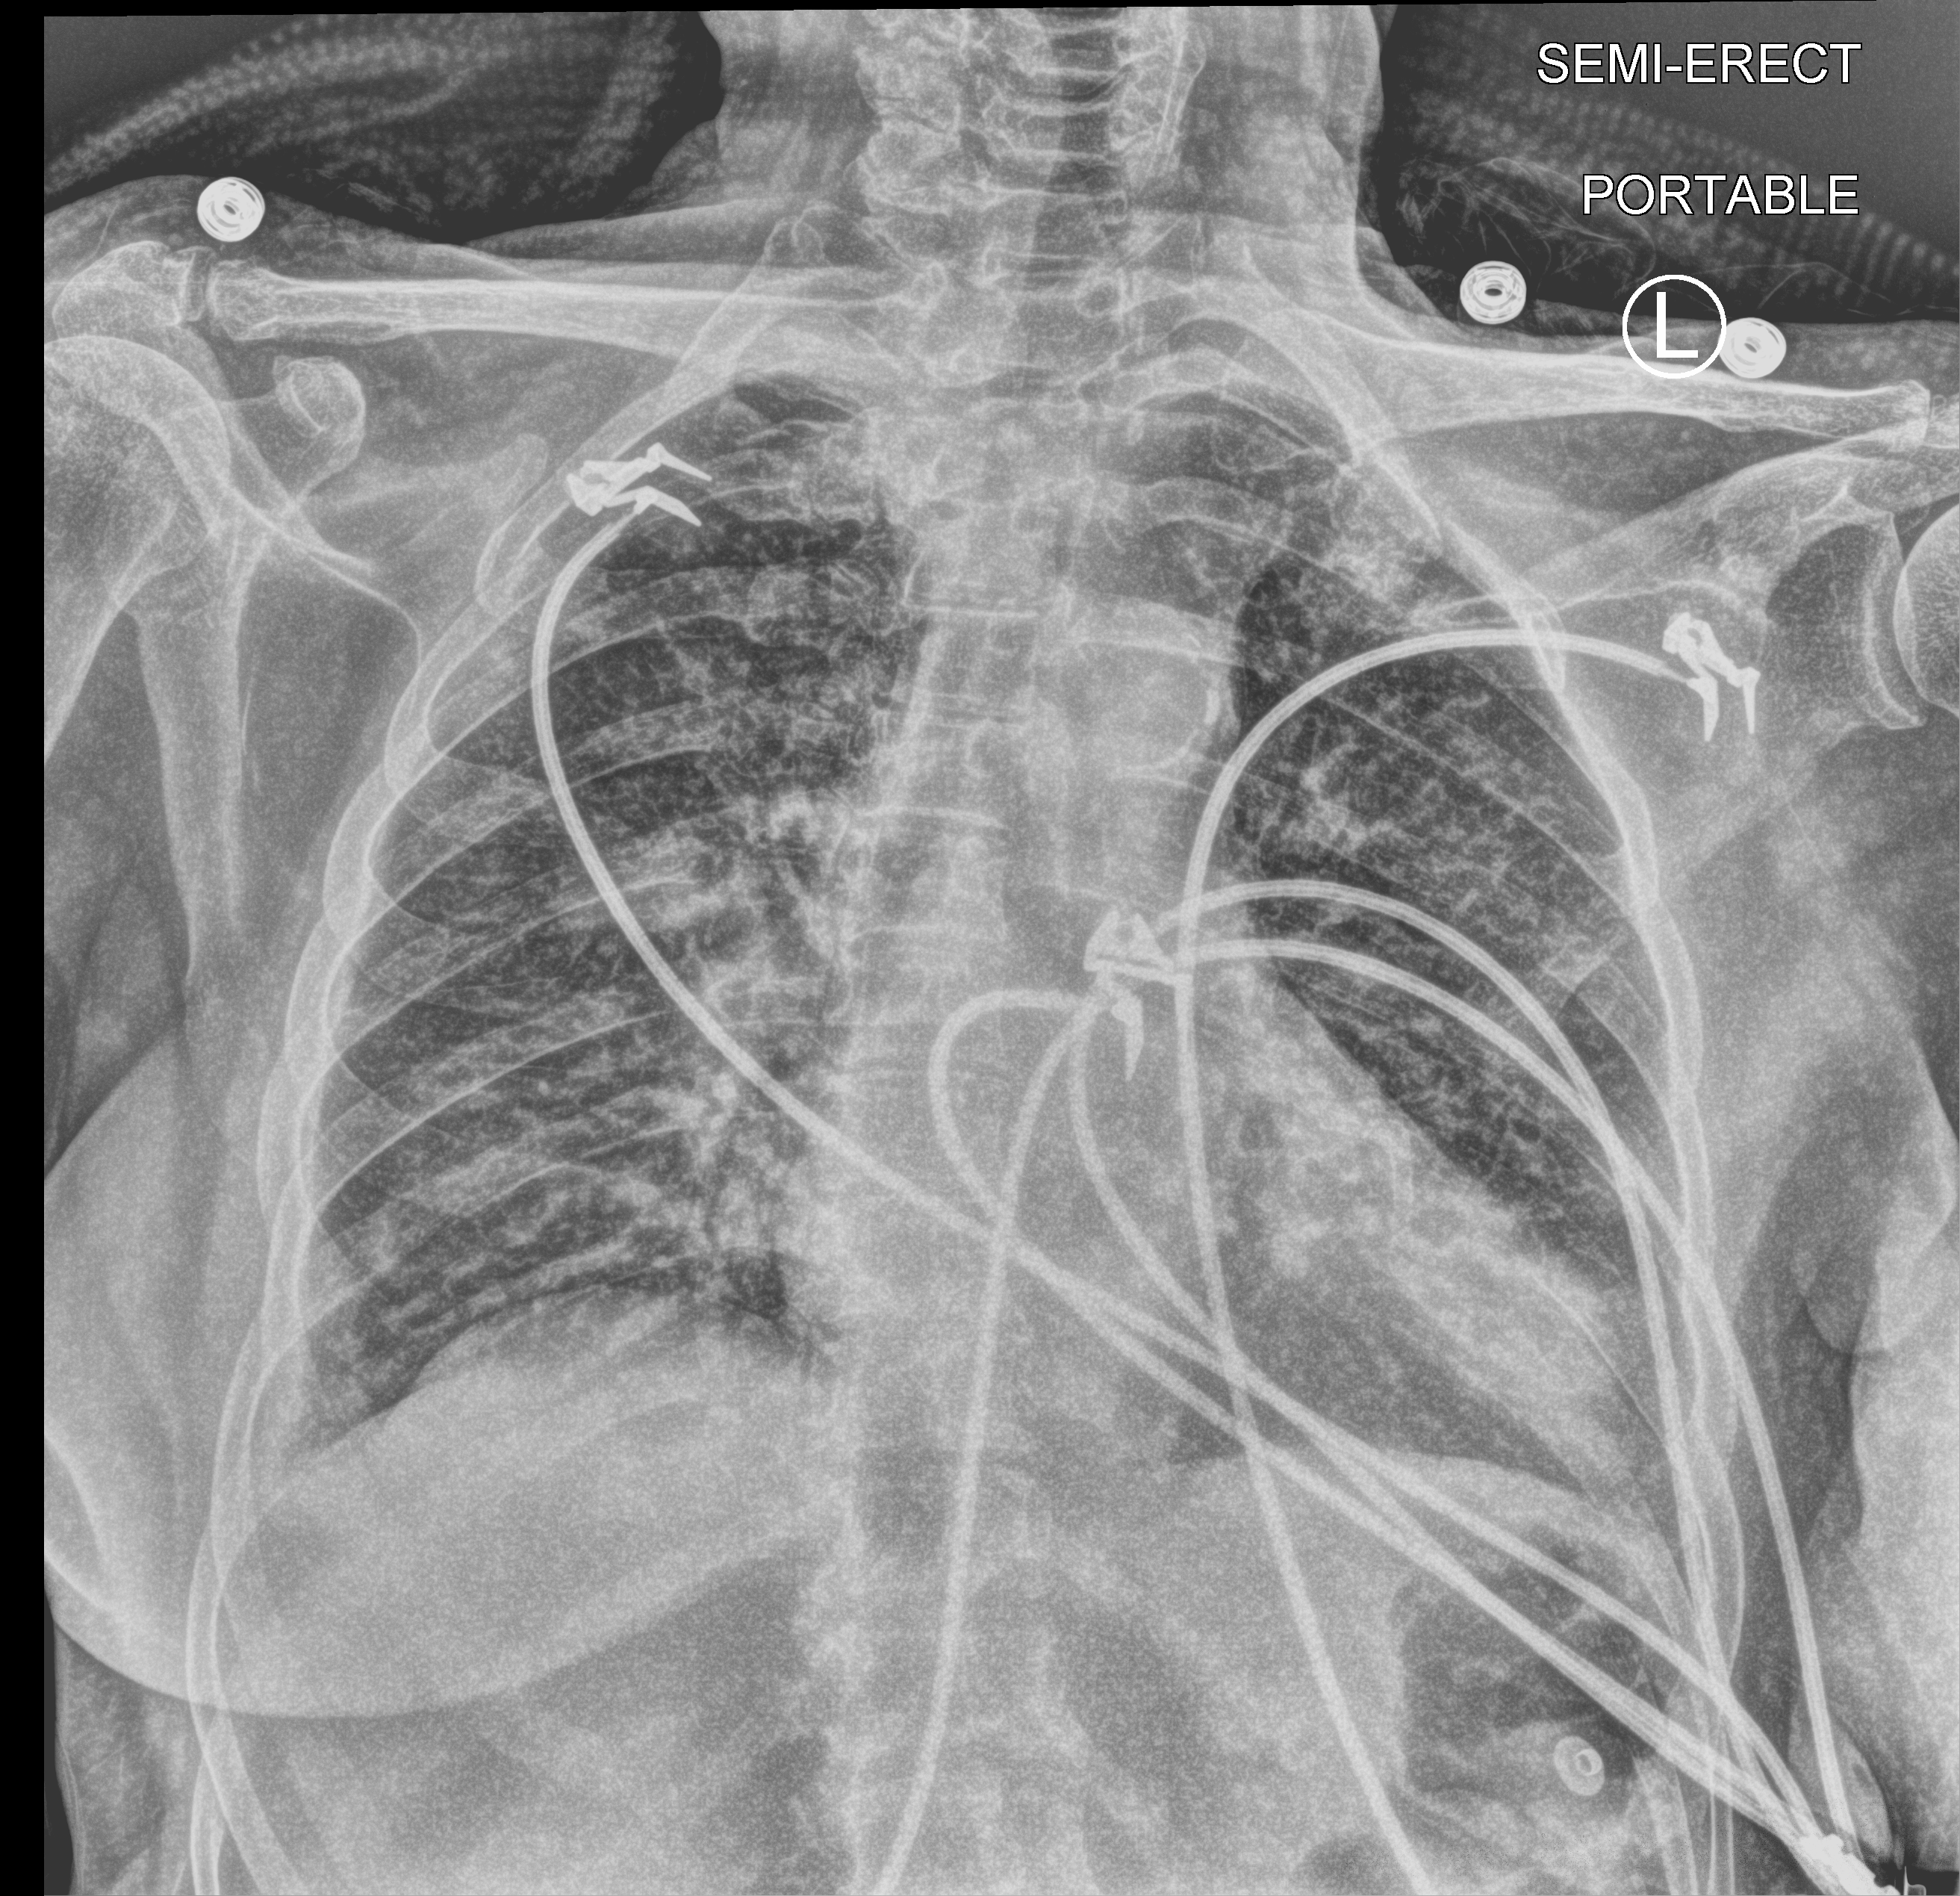
Portable chest radiograph, anteroposterior (AP) projection. Patient hospitalised with COVID-19; female, aged 60–74 years.
Admission-level facts for this patient (not findings on this image; timing relative to this image not recorded): smoking status (admission record): never.